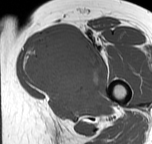
MRI of an extremity soft-tissue mass, one axial slice; position 38 of 57 along the scan axis; MR volume resampled by the dataset authors to the PET/CT grid (not the native acquisition matrix); 3.27 mm slice thickness; 152 × 144 image matrix, field of view 148 × 141 mm. Female patient. Case-level facts recorded for this patient, not image findings: histological type: pleiomorphic leiomyosarcoma; grade: intermediate; site of the primary tumour: left thigh.
Annotated regions visible in this slice (expert contour drawn on MRI and transferred to this co-registered scan by the dataset authors):
- gross tumour volume including surrounding oedema: bounding box [x1, y1, x2, y2] px = [22, 30, 103, 98]
- gross tumour volume (mass): [22, 30, 103, 98]